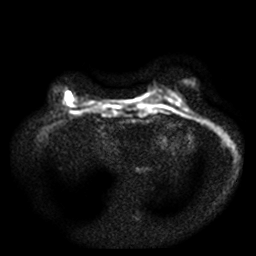
Breast MRI, one axial slice. Diffusion-weighted series; image 2 of 4 stored at this slice position (different b-values; order by instance number). 3 T. 5 mm slice thickness. 256 × 256 image matrix, field of view 340 × 340 mm. Female patient.
Outlined on this slice (manually delineated by an expert):
- tumour on diffusion-weighted imaging: box from (x=66, y=91) to (x=72, y=101) px